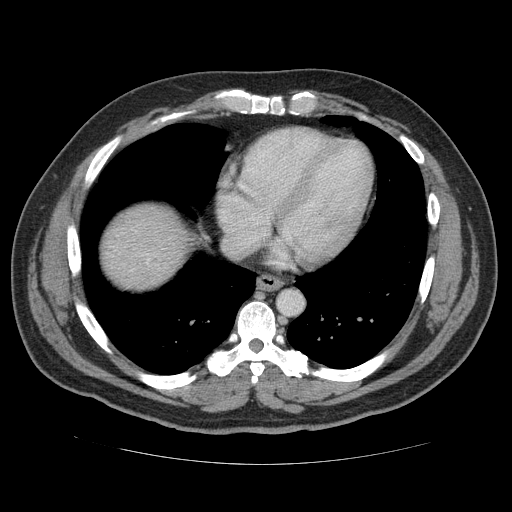
Contrast-enhanced abdominal CT (liver protocol), one axial slice. Position 110 of 113 along the scan axis. Reconstruction kernel STANDARD. Soft-tissue window (W 400 / L 40 HU). 2.5 mm slice thickness. 512 × 512 image matrix. From the clinical record (not read from this slice): diagnosis: hepatocellular carcinoma (patient treated with transarterial chemoembolisation; whether this scan precedes or follows treatment is not stated here); TNM stage (as recorded): Stage-II; Child-Pugh class: B; tumour differentiation: moderately differentiated; tumour nodularity: multinodular.
Outlined on this slice (semi-automatically segmented with operator editing):
- liver parenchyma outside the tumour (the mass and vessels are separate outlines, so this box may not span the whole liver): bounding box <104,209,178,280> (left, top, right, bottom; pixels)